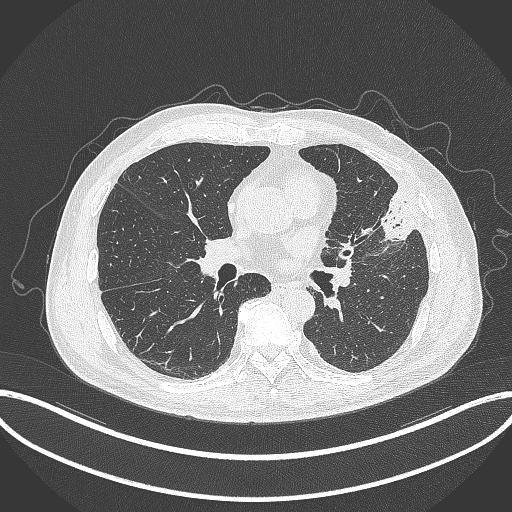
Chest CT, one axial slice. Slice 170 of 382 in the series (ordered by position). 120 kVp. Lung window (W 1500 / L -600 HU). 512 × 512 image matrix, field of view 415 × 415 mm. Male patient, age 64 years. From the clinical record (not read from this slice): clinical TNM (as recorded): T4 N1 M0; histopathological grade: G3.
Structures marked on this image (rectangle marked by the reading radiologist):
- lung tumour (recorded histology: adenocarcinoma): box from (x=373, y=185) to (x=417, y=243) px